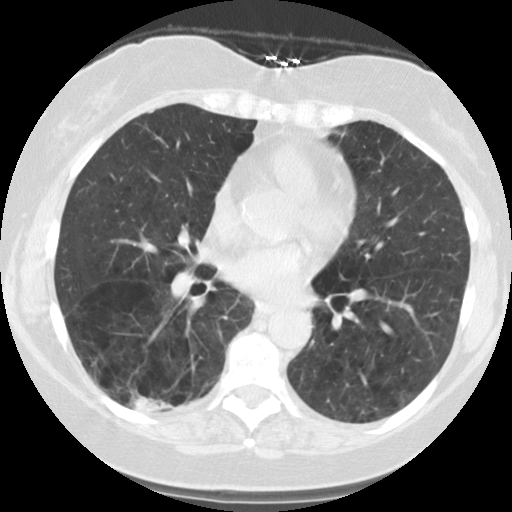
Low-dose screening chest CT, one axial slice; slice 55 of 122 in the series (ordered by position); reconstruction kernel STANDARD; 140 kVp; lung window (W 1500 / L -600 HU); 2.5 mm slice thickness; 512 × 512 image matrix, field of view 310 × 310 mm.
Annotated regions visible in this slice (expert manual segmentation):
- lesion 1 (tumor, lower lobe of right lung): bounding box (x1, y1, x2, y2) in pixels: (132, 394, 175, 413)